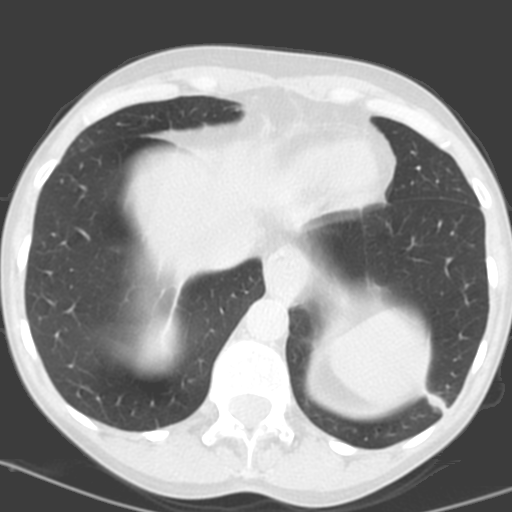
Low-dose screening chest CT, one axial slice. Position 38 of 156 along the scan axis. Lung window (W 1500 / L -600 HU). 3.2 mm slice thickness. 512 × 512 image matrix, field of view 262 × 262 mm.
Structures marked on this image (outlined manually by an expert reader):
- lesion 1 (tumor, lower lobe of left lung): box from (x=428, y=393) to (x=446, y=412) px